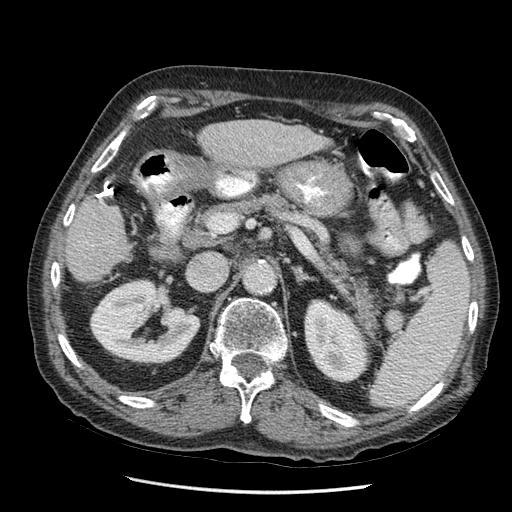
Contrast-enhanced abdominal CT (liver protocol), one axial slice; slice 19 of 67 in the series (ordered by position); reconstruction kernel STANDARD; soft-tissue window (W 400 / L 40 HU); 2.5 mm slice thickness; 512 × 512 image matrix, field of view 360 × 360 mm. Case-level facts recorded for this patient, not image findings: diagnosis: hepatocellular carcinoma (patient treated with transarterial chemoembolisation; whether this scan precedes or follows treatment is not stated here); TNM stage (as recorded): Stage-I; Child-Pugh class: A; tumour nodularity: uninodular.
Annotated regions visible in this slice (semi-automatic segmentation, software-assisted and operator-edited):
- liver parenchyma outside the tumour (the mass and vessels are separate outlines, so this box may not span the whole liver): bounding box [x1, y1, x2, y2] px = [66, 120, 332, 286]
- liver vessels: [90, 196, 114, 245]